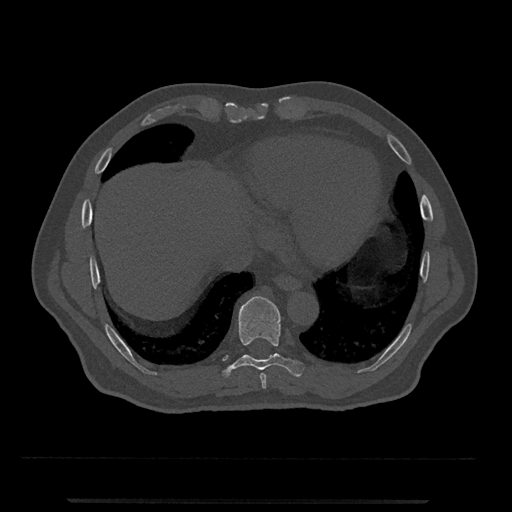
CT including the spine, one axial slice. Slice 573 of 797 in the series (ordered by position). Reconstruction kernel Br40s/3. 120 kVp. Bone window (W 1800 / L 400 HU). 0.5 mm slice thickness. 512 × 512 image matrix. Male patient, age 63 years. From the clinical record (not read from this slice): primary cancer: prostate.
Outlined on this slice (semi-automatic segmentation, software-assisted and operator-edited):
- T8 vertebra: bounding box (x1, y1, x2, y2) in pixels: (259, 373, 267, 389)
- T9 vertebra: (222, 296, 304, 377)